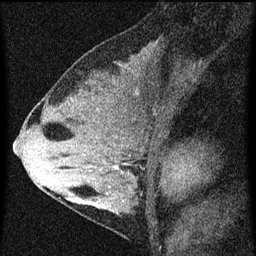
Breast MRI (dynamic contrast-enhanced), one sagittal slice. Position 33 of 60 along the scan axis. Dynamic contrast-enhanced series, image 2 of 3 at this slice position (ordered by acquisition). 1.5 T. TE 4.2 ms, TR 8 ms. 256 × 256 image matrix, field of view 180 × 180 mm. Patient: female, 33 years.
Annotated regions visible in this slice (semi-automatically segmented with operator editing):
- analysis volume of interest (the breast-tissue region the enhancement analysis was run in; not a lesion): bounding box (x1, y1, x2, y2) in pixels: (67, 118, 161, 215)
- tumour enhancement mask (voxels above the 70 % enhancement threshold inside the analysis volume of interest): (113, 166, 119, 169)